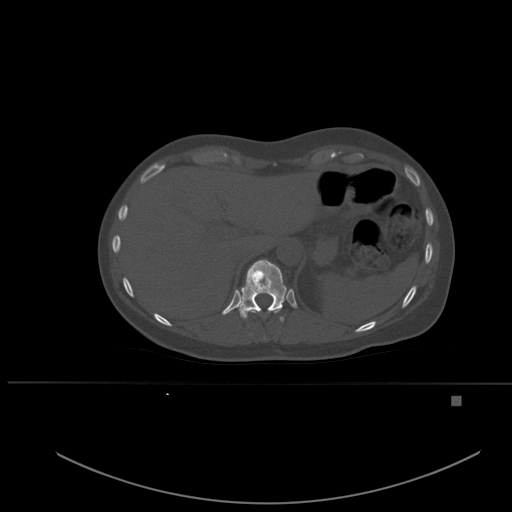
CT including the spine, one axial slice. Slice 277 of 651 in the series (ordered by position). Bone window (W 1800 / L 400 HU). 1.5 mm slice thickness. 512 × 512 image matrix, field of view 443 × 443 mm. Patient: female, 49 years. From the clinical record (not read from this slice): primary cancer: breast.
Annotated regions visible in this slice (semi-automatic segmentation, software-assisted and operator-edited):
- T10 vertebra: box from (x=245, y=308) to (x=282, y=317) px
- T11 vertebra: (x=237, y=259)–(x=287, y=322)